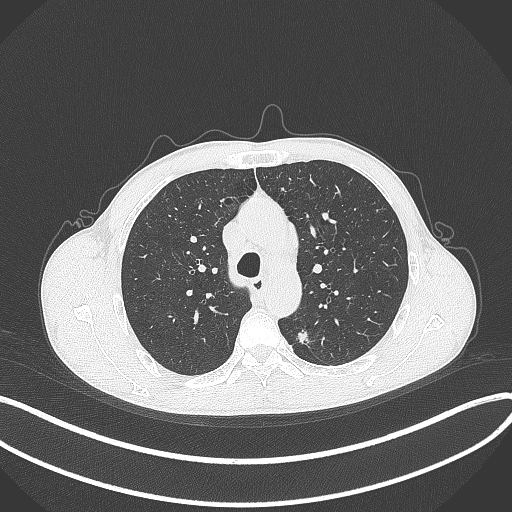
Chest CT, one axial slice. Position 279 of 429 along the scan axis. Reconstruction kernel B70f. 120 kVp. Lung window (W 1500 / L -600 HU). 512 × 512 image matrix, field of view 400 × 400 mm. Male patient, age 51 years. From the clinical record (not read from this slice): clinical TNM (as recorded): T2a N1 M1.
Outlined on this slice (rectangle marked by the reading radiologist):
- lung tumour (recorded histology: adenocarcinoma): bounding box (x1, y1, x2, y2) in pixels: (295, 325, 314, 349)